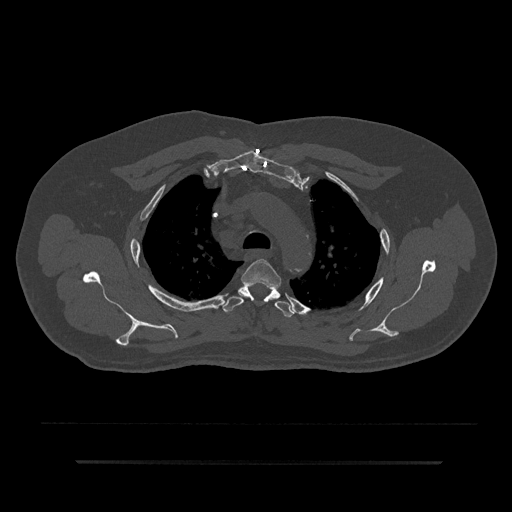
CT including the spine, one axial slice; position 638 of 797 along the scan axis; reconstruction kernel Br40s/3; 120 kVp; bone window (W 1800 / L 400 HU); 0.5 mm slice thickness; 512 × 512 image matrix, field of view 464 × 464 mm. Male patient, age 59 years. From the clinical record (not read from this slice): primary cancer: bile ducts; vertebrae with lytic lesions (as recorded): T10.
Annotated regions visible in this slice (semi-automatically segmented with operator editing):
- T3 vertebra: box from (x=241, y=259) to (x=282, y=288) px
- T4 vertebra: (x=222, y=284)–(x=294, y=317)